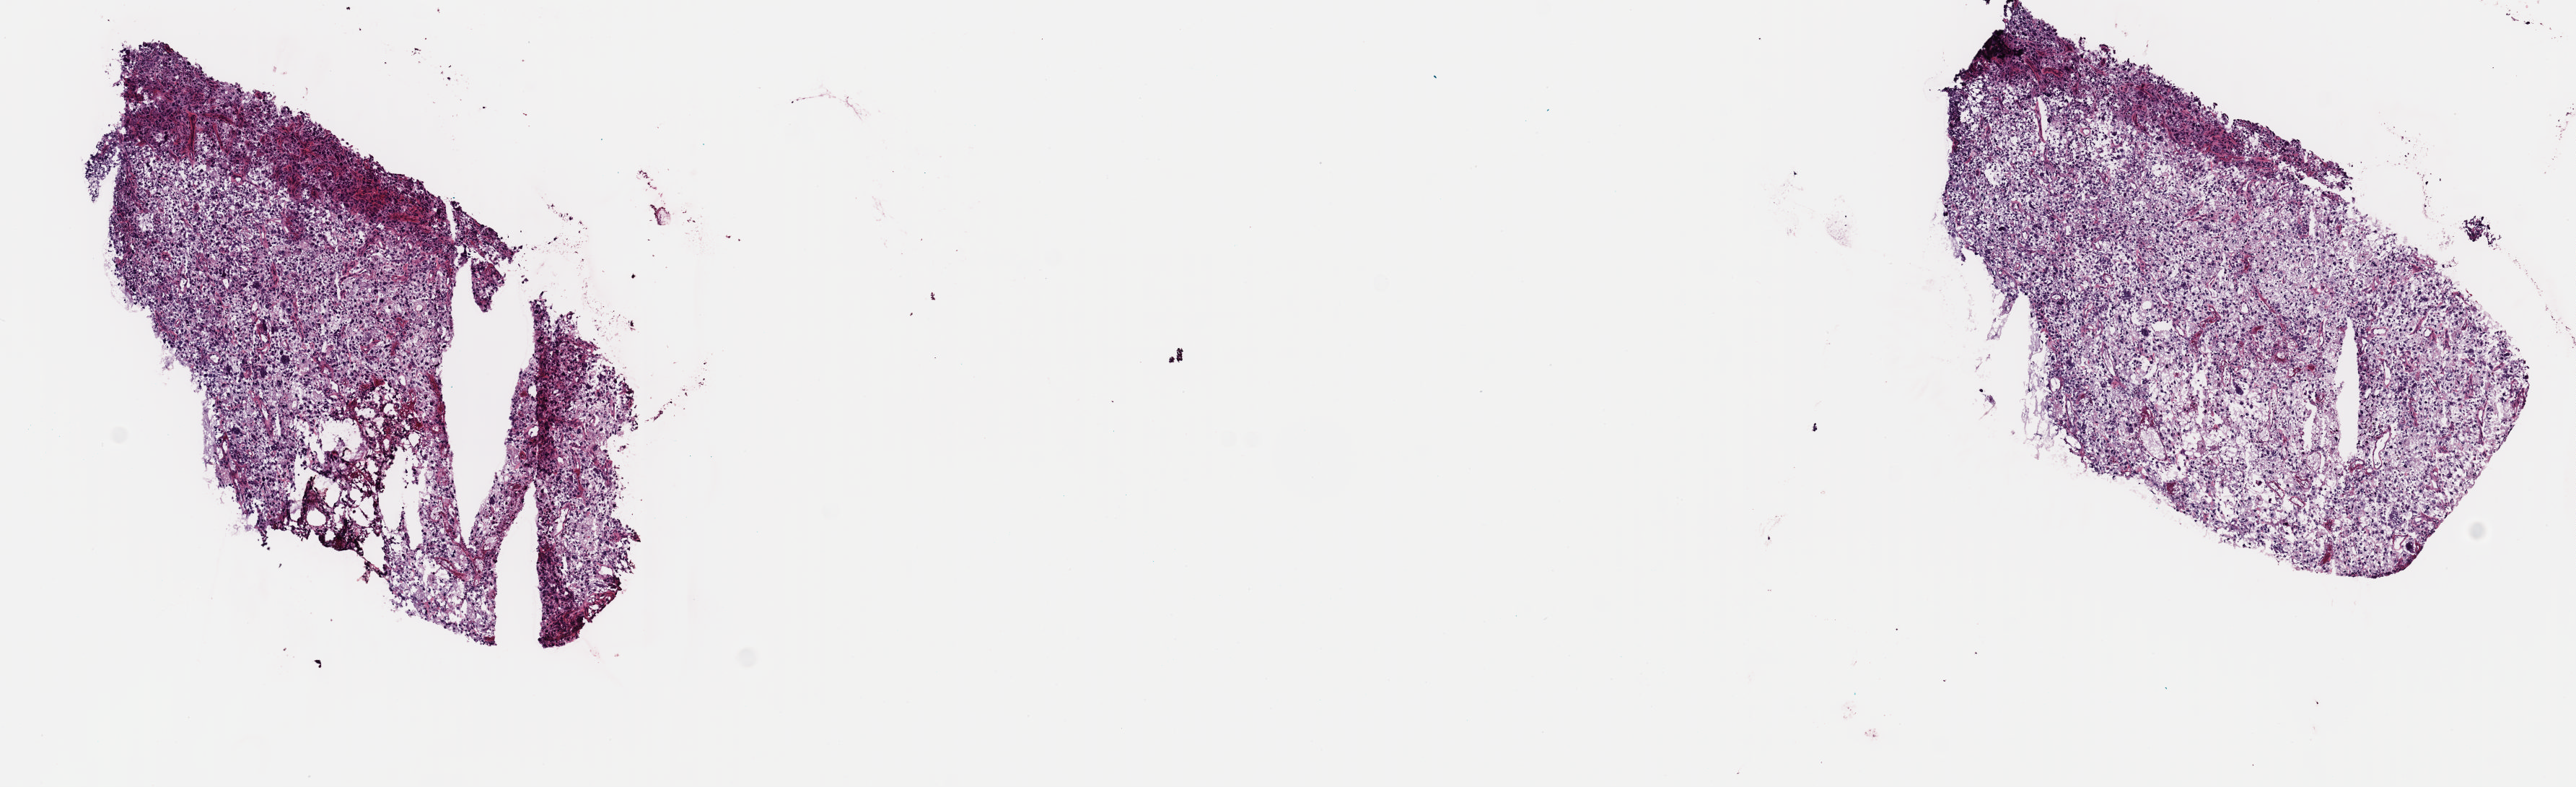
Digitized Hematoxylin and eosin (H&E) stained tissue section (whole slide), shown as a low-resolution overview of the whole scanned area (about 14.1 x 4.3 mm), frozen section from the top of the tissue portion, connective, subcutaneous and other soft tissues, primary tumour sample. Female patient; age at initial diagnosis 78 years. Slide review estimates, as recorded: tumour cells 60%, tumour nuclei 100%, normal cells 0%, stromal cells 40%, necrosis 0%. Infiltration values recorded for this section: lymphocyte infiltration 0%, monocyte infiltration 0%, neutrophil infiltration 0%.
* diagnosis: Undifferentiated sarcoma